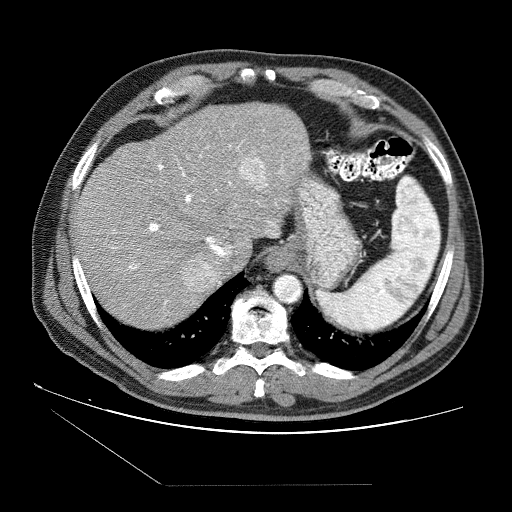
Contrast-enhanced abdominal CT (liver protocol), one axial slice. Slice 64 of 87 in the series (ordered by position). Soft-tissue window (W 400 / L 40 HU). 2.5 mm slice thickness. 512 × 512 image matrix, field of view 400 × 400 mm. Case-level facts recorded for this patient, not image findings: diagnosis: hepatocellular carcinoma (patient treated with transarterial chemoembolisation; whether this scan precedes or follows treatment is not stated here); TNM stage (as recorded): Stage-II; Child-Pugh class: B; tumour differentiation: no biopsy; tumour nodularity: multinodular.
Structures marked on this image (semi-automatic segmentation, software-assisted and operator-edited):
- liver parenchyma outside the tumour (the mass and vessels are separate outlines, so this box may not span the whole liver): bounding box <76,102,310,328> (left, top, right, bottom; pixels)
- mass: <180,155,266,294>
- liver vessels: <112,136,304,305>